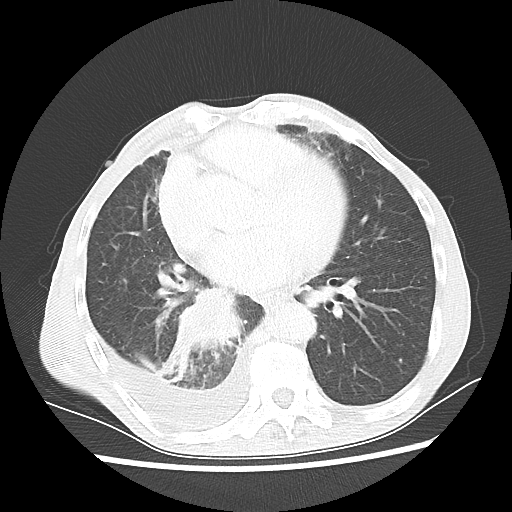
Chest CT, one axial slice. Slice 26 of 60 in the series (ordered by position). Reconstruction kernel LUNG. 80 kVp. Lung window (W 1500 / L -600 HU). 512 × 512 image matrix, field of view 335 × 335 mm. Patient: male, 76 years. Case-level facts recorded for this patient, not image findings: clinical TNM (as recorded): T3 N3 M1a.
Annotated regions visible in this slice (bounding box drawn by a radiologist):
- lung tumour (recorded histology: squamous cell carcinoma): bounding box [x1, y1, x2, y2] px = [151, 283, 245, 385]